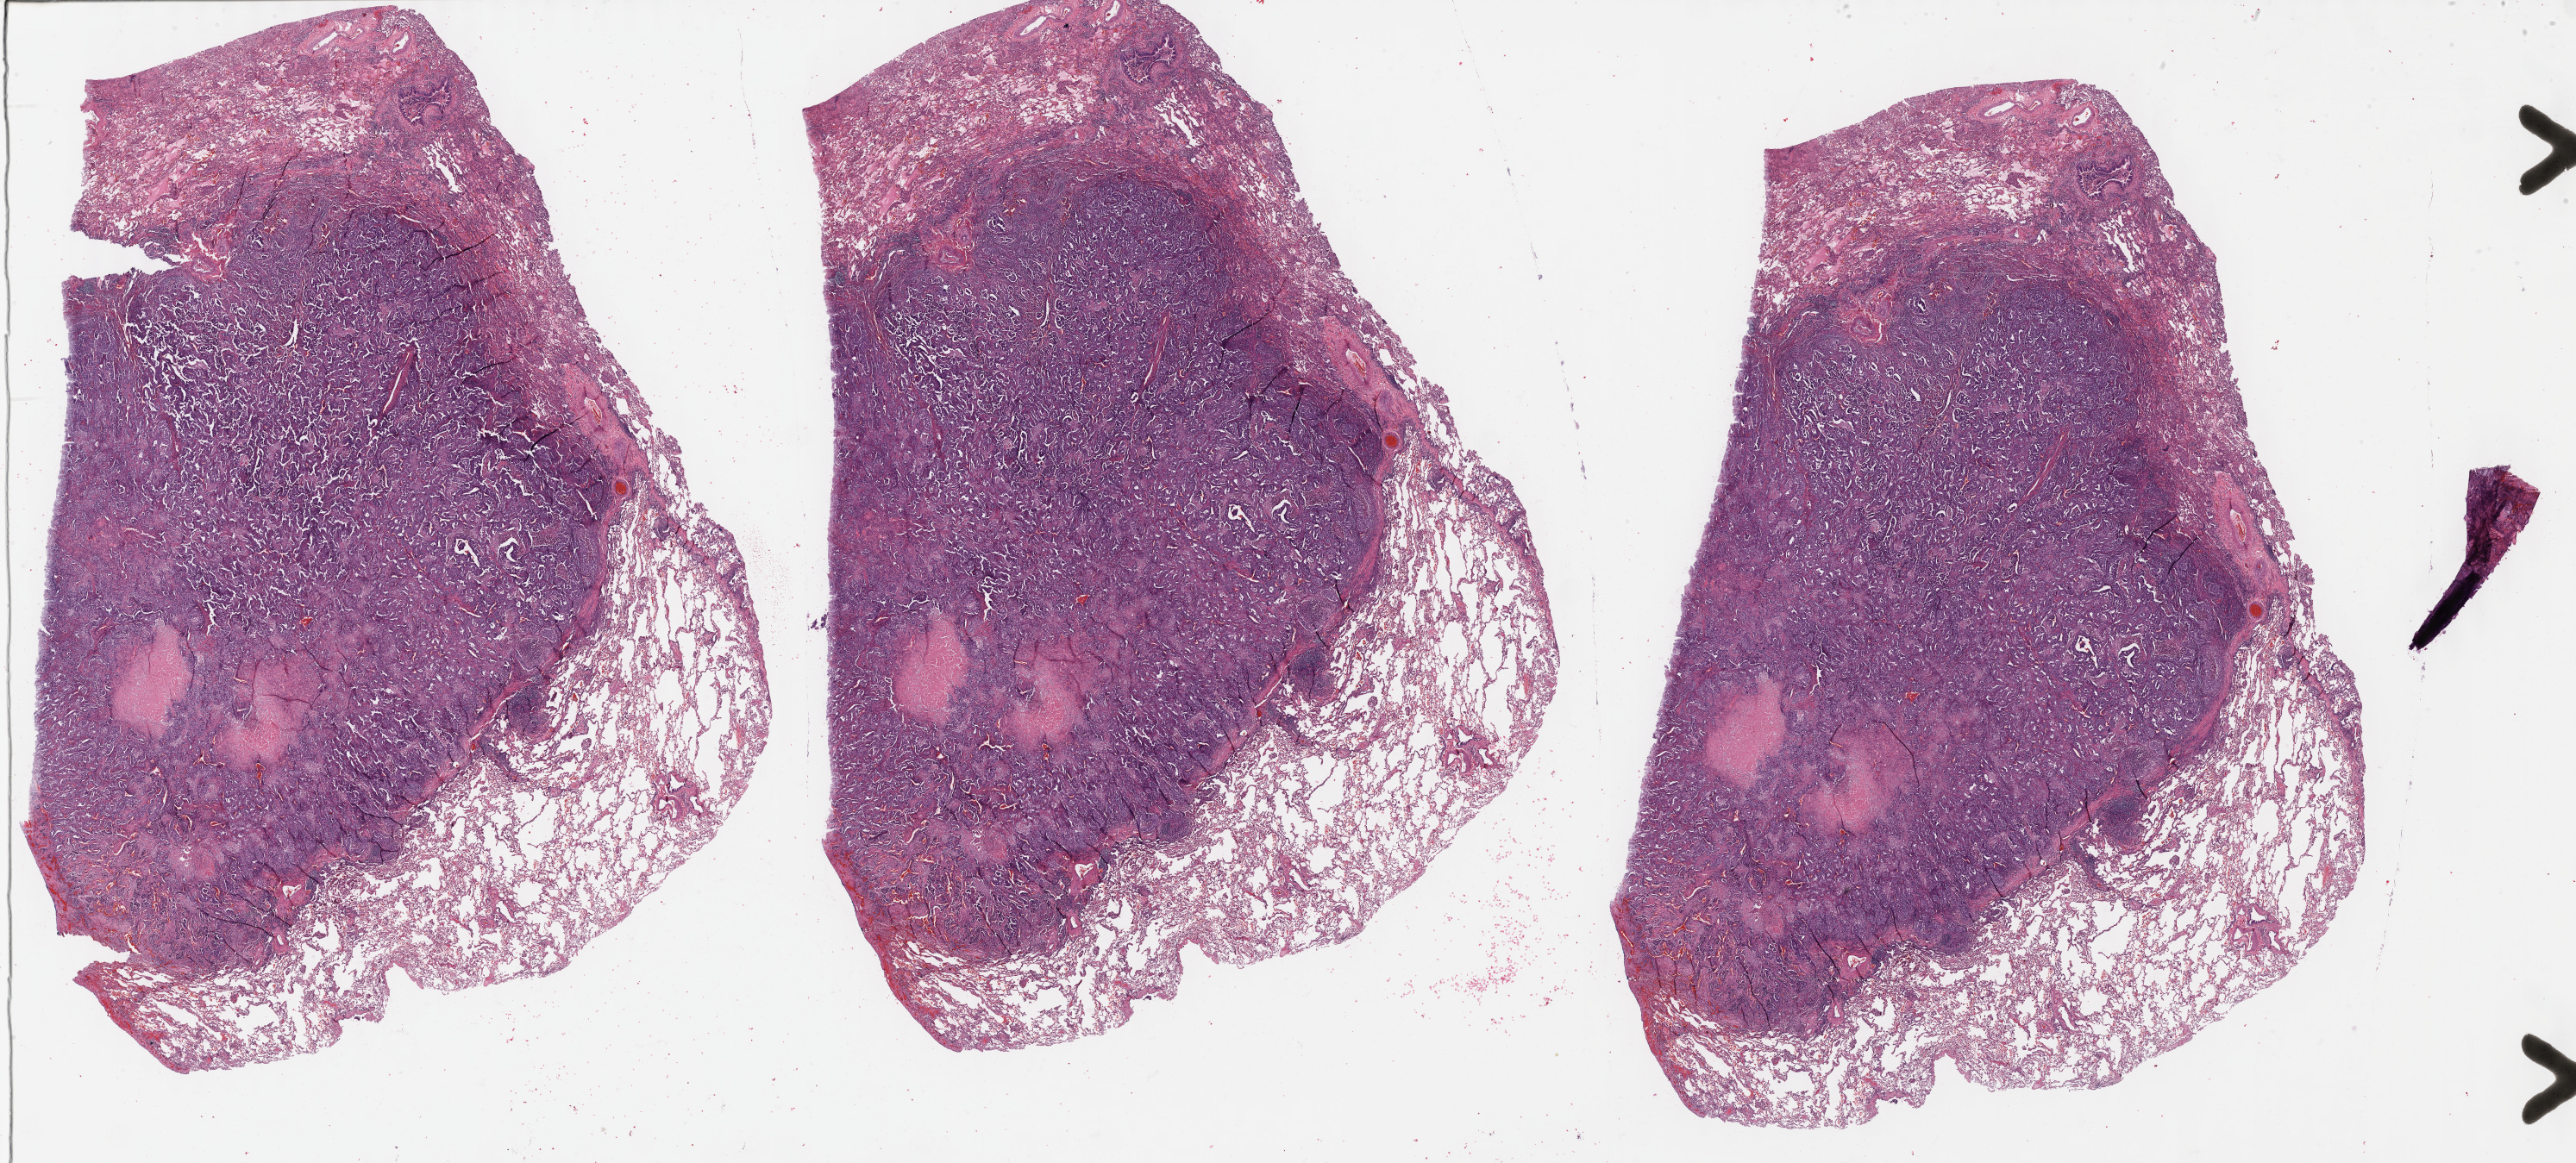
Digitized H&E tissue section (whole slide), a low-resolution overview of the entire scanned area, about 48.3 x 21.8 mm (slide scanned at 40x); formalin-fixed paraffin-embedded (FFPE) diagnostic section; sample: primary tumour, lung. Female, age 50 years at initial diagnosis.
Diagnosis: Adenocarcinoma with mixed subtypes (upper lobe, lung). AJCC pathologic stage: IA (6th edition). Laterality: right. TNM: T1 N0 M0.